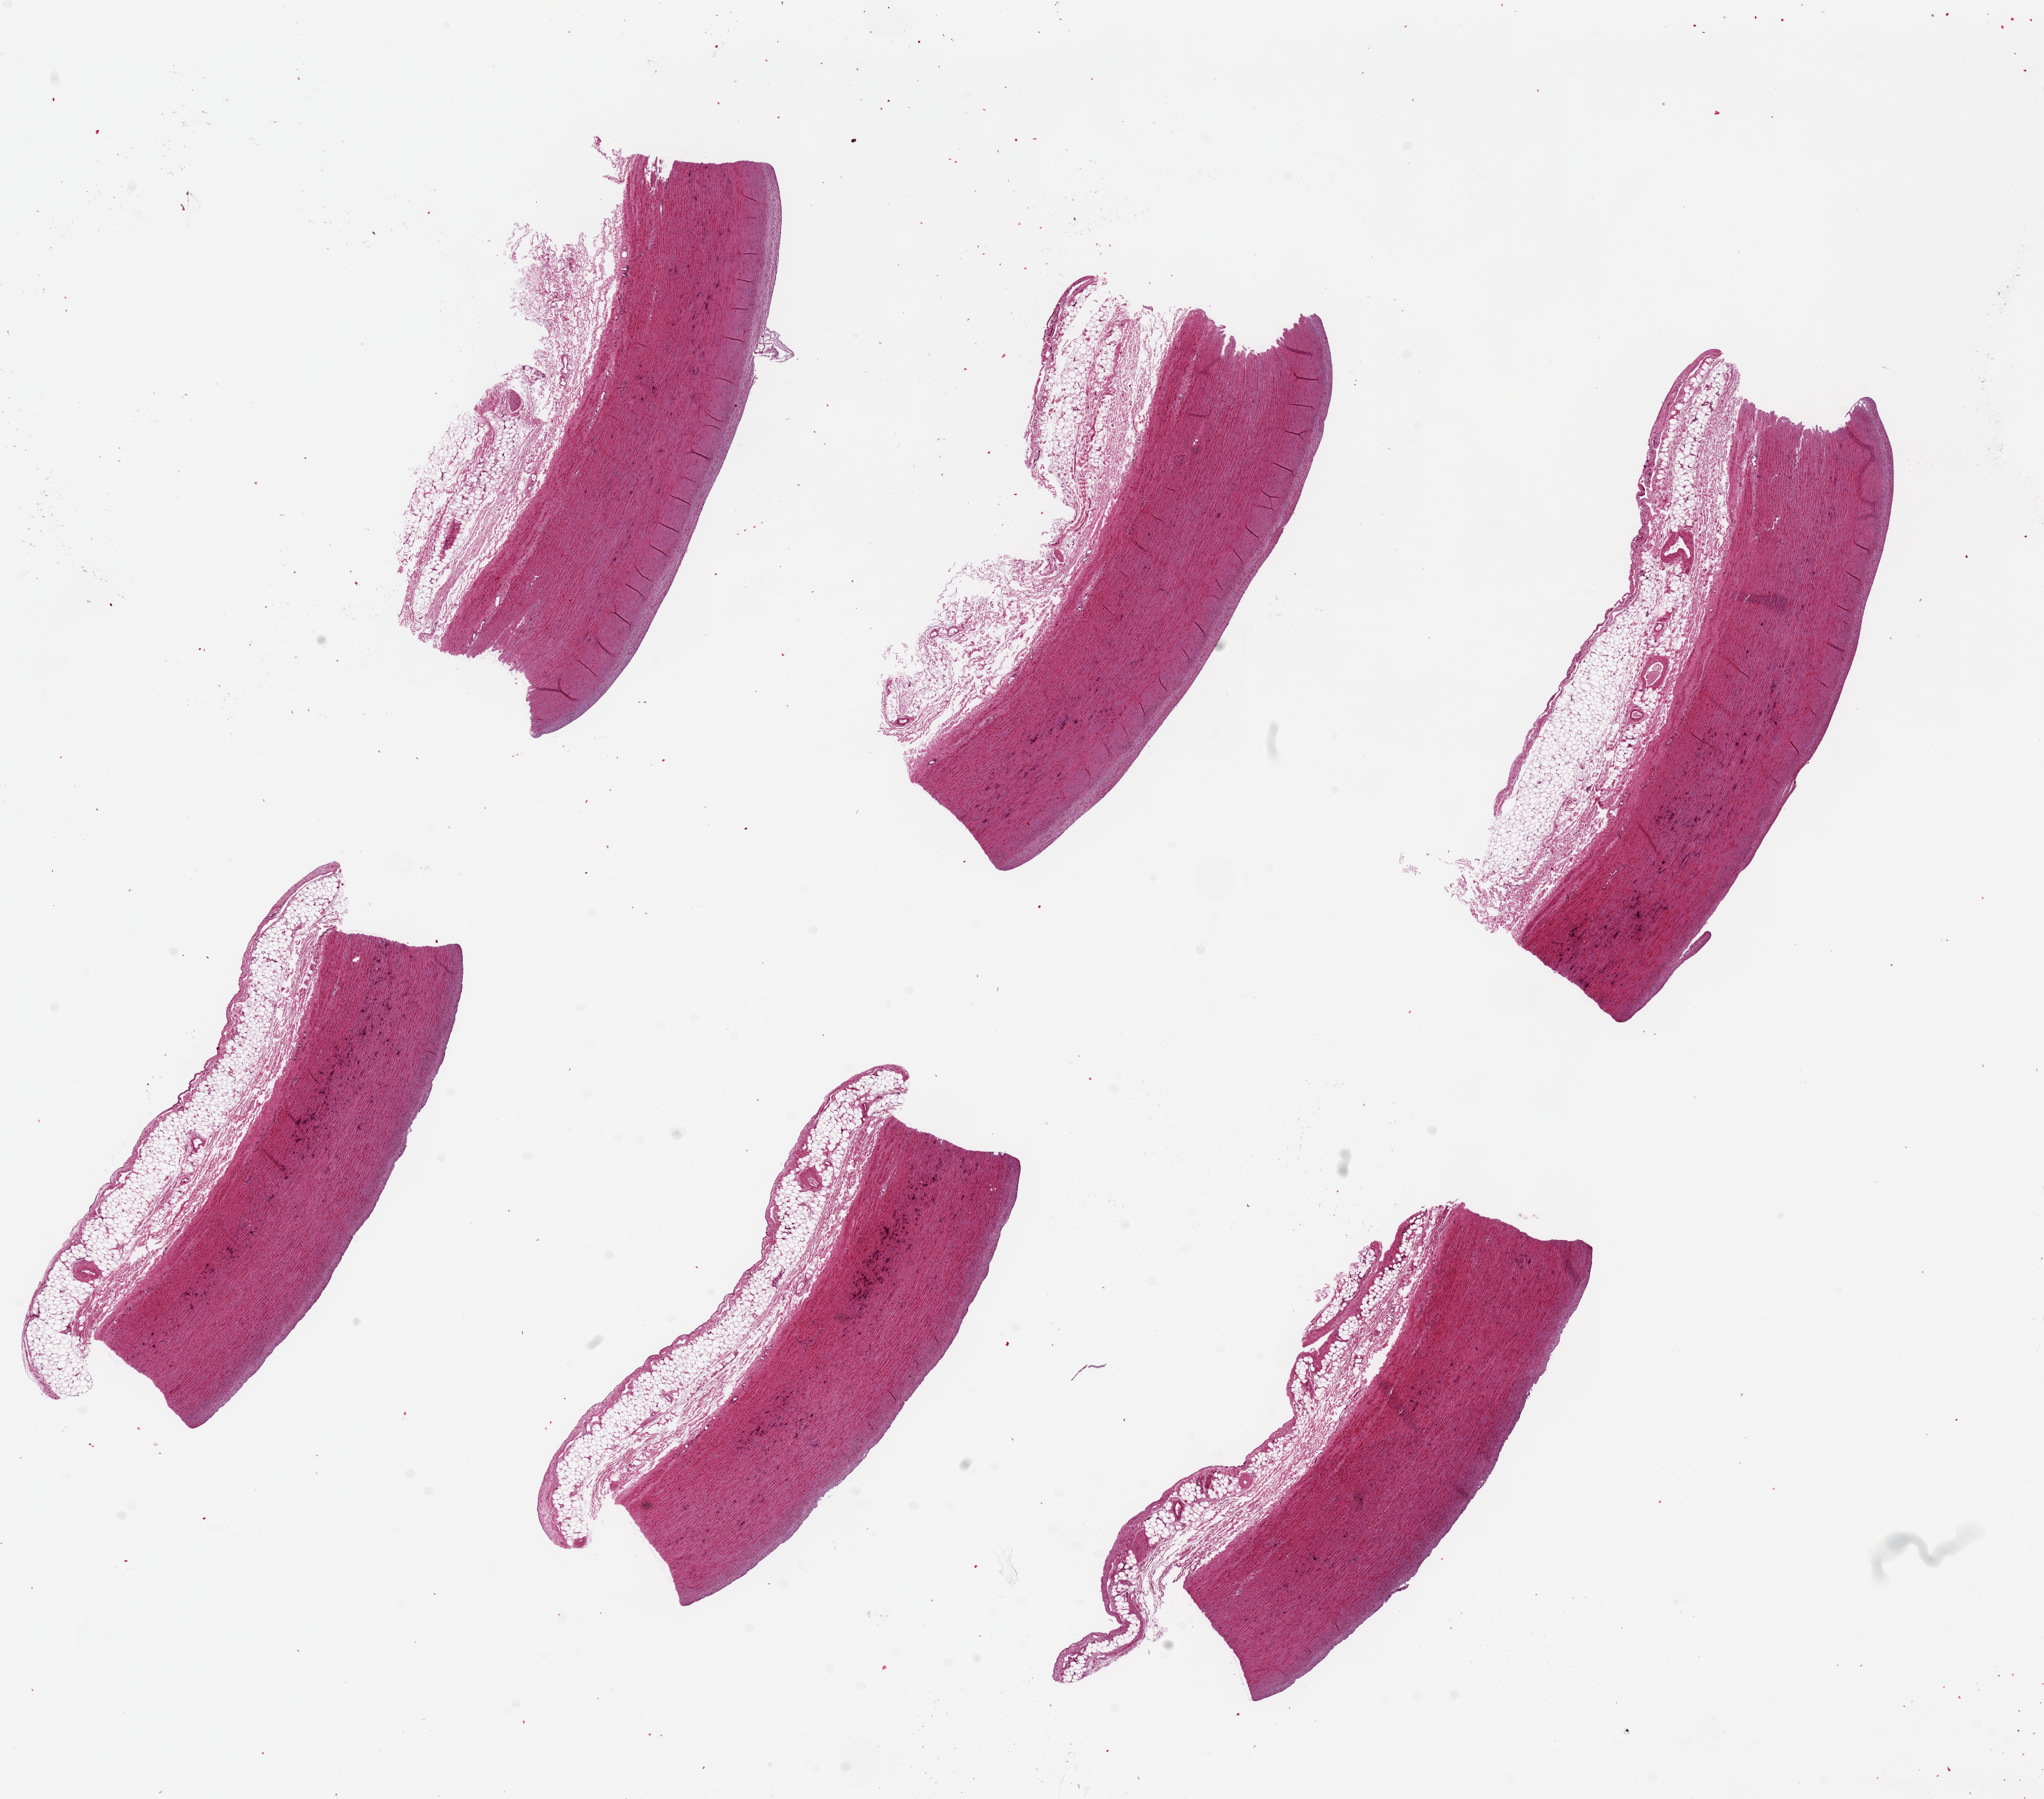
Whole-slide image, H&E stain — a low-resolution overview of the entire scanned area, about 22.6 x 19.9 mm; PAXgene-fixed, paraffin-embedded tissue; sampled site (target tissue): aorta; donor tissue sample. Male donor.
- review note (as recorded): 6 pieces, up to 7x3mm; preserved endothelium, punctate medial calcification, 1 mm adventitial adipose on all sides